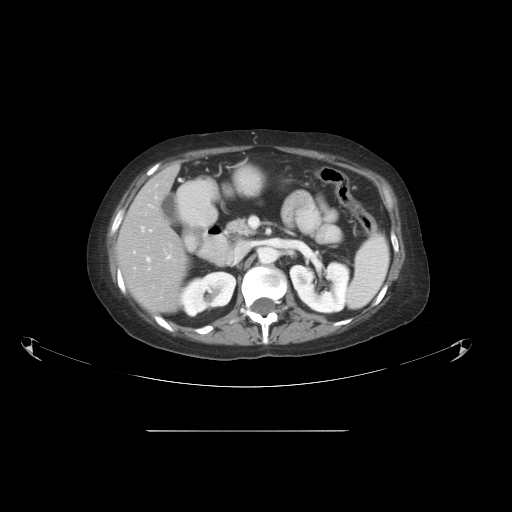
Contrast-enhanced abdominal CT, one axial slice; slice 28 of 51 in the series (ordered by position); intravenous contrast given; soft-tissue window (W 400 / L 40 HU); 512 × 512 image matrix. Female patient, age 48 years. From the clinical record (not read from this slice): diagnosis: colorectal cancer liver metastases, imaged before liver resection; multiple liver metastases: yes; largest metastasis: 1 cm; chemotherapy before resection: no.
Outlined on this slice (manually delineated by an expert):
- hepatic veins: box from (x=147, y=255) to (x=171, y=270) px
- liver: (x=117, y=166)–(x=188, y=313)
- planned liver remnant (the part of the liver to remain after resection): (x=117, y=166)–(x=189, y=313)
- portal vein (with intrahepatic branches): (x=133, y=204)–(x=152, y=254)